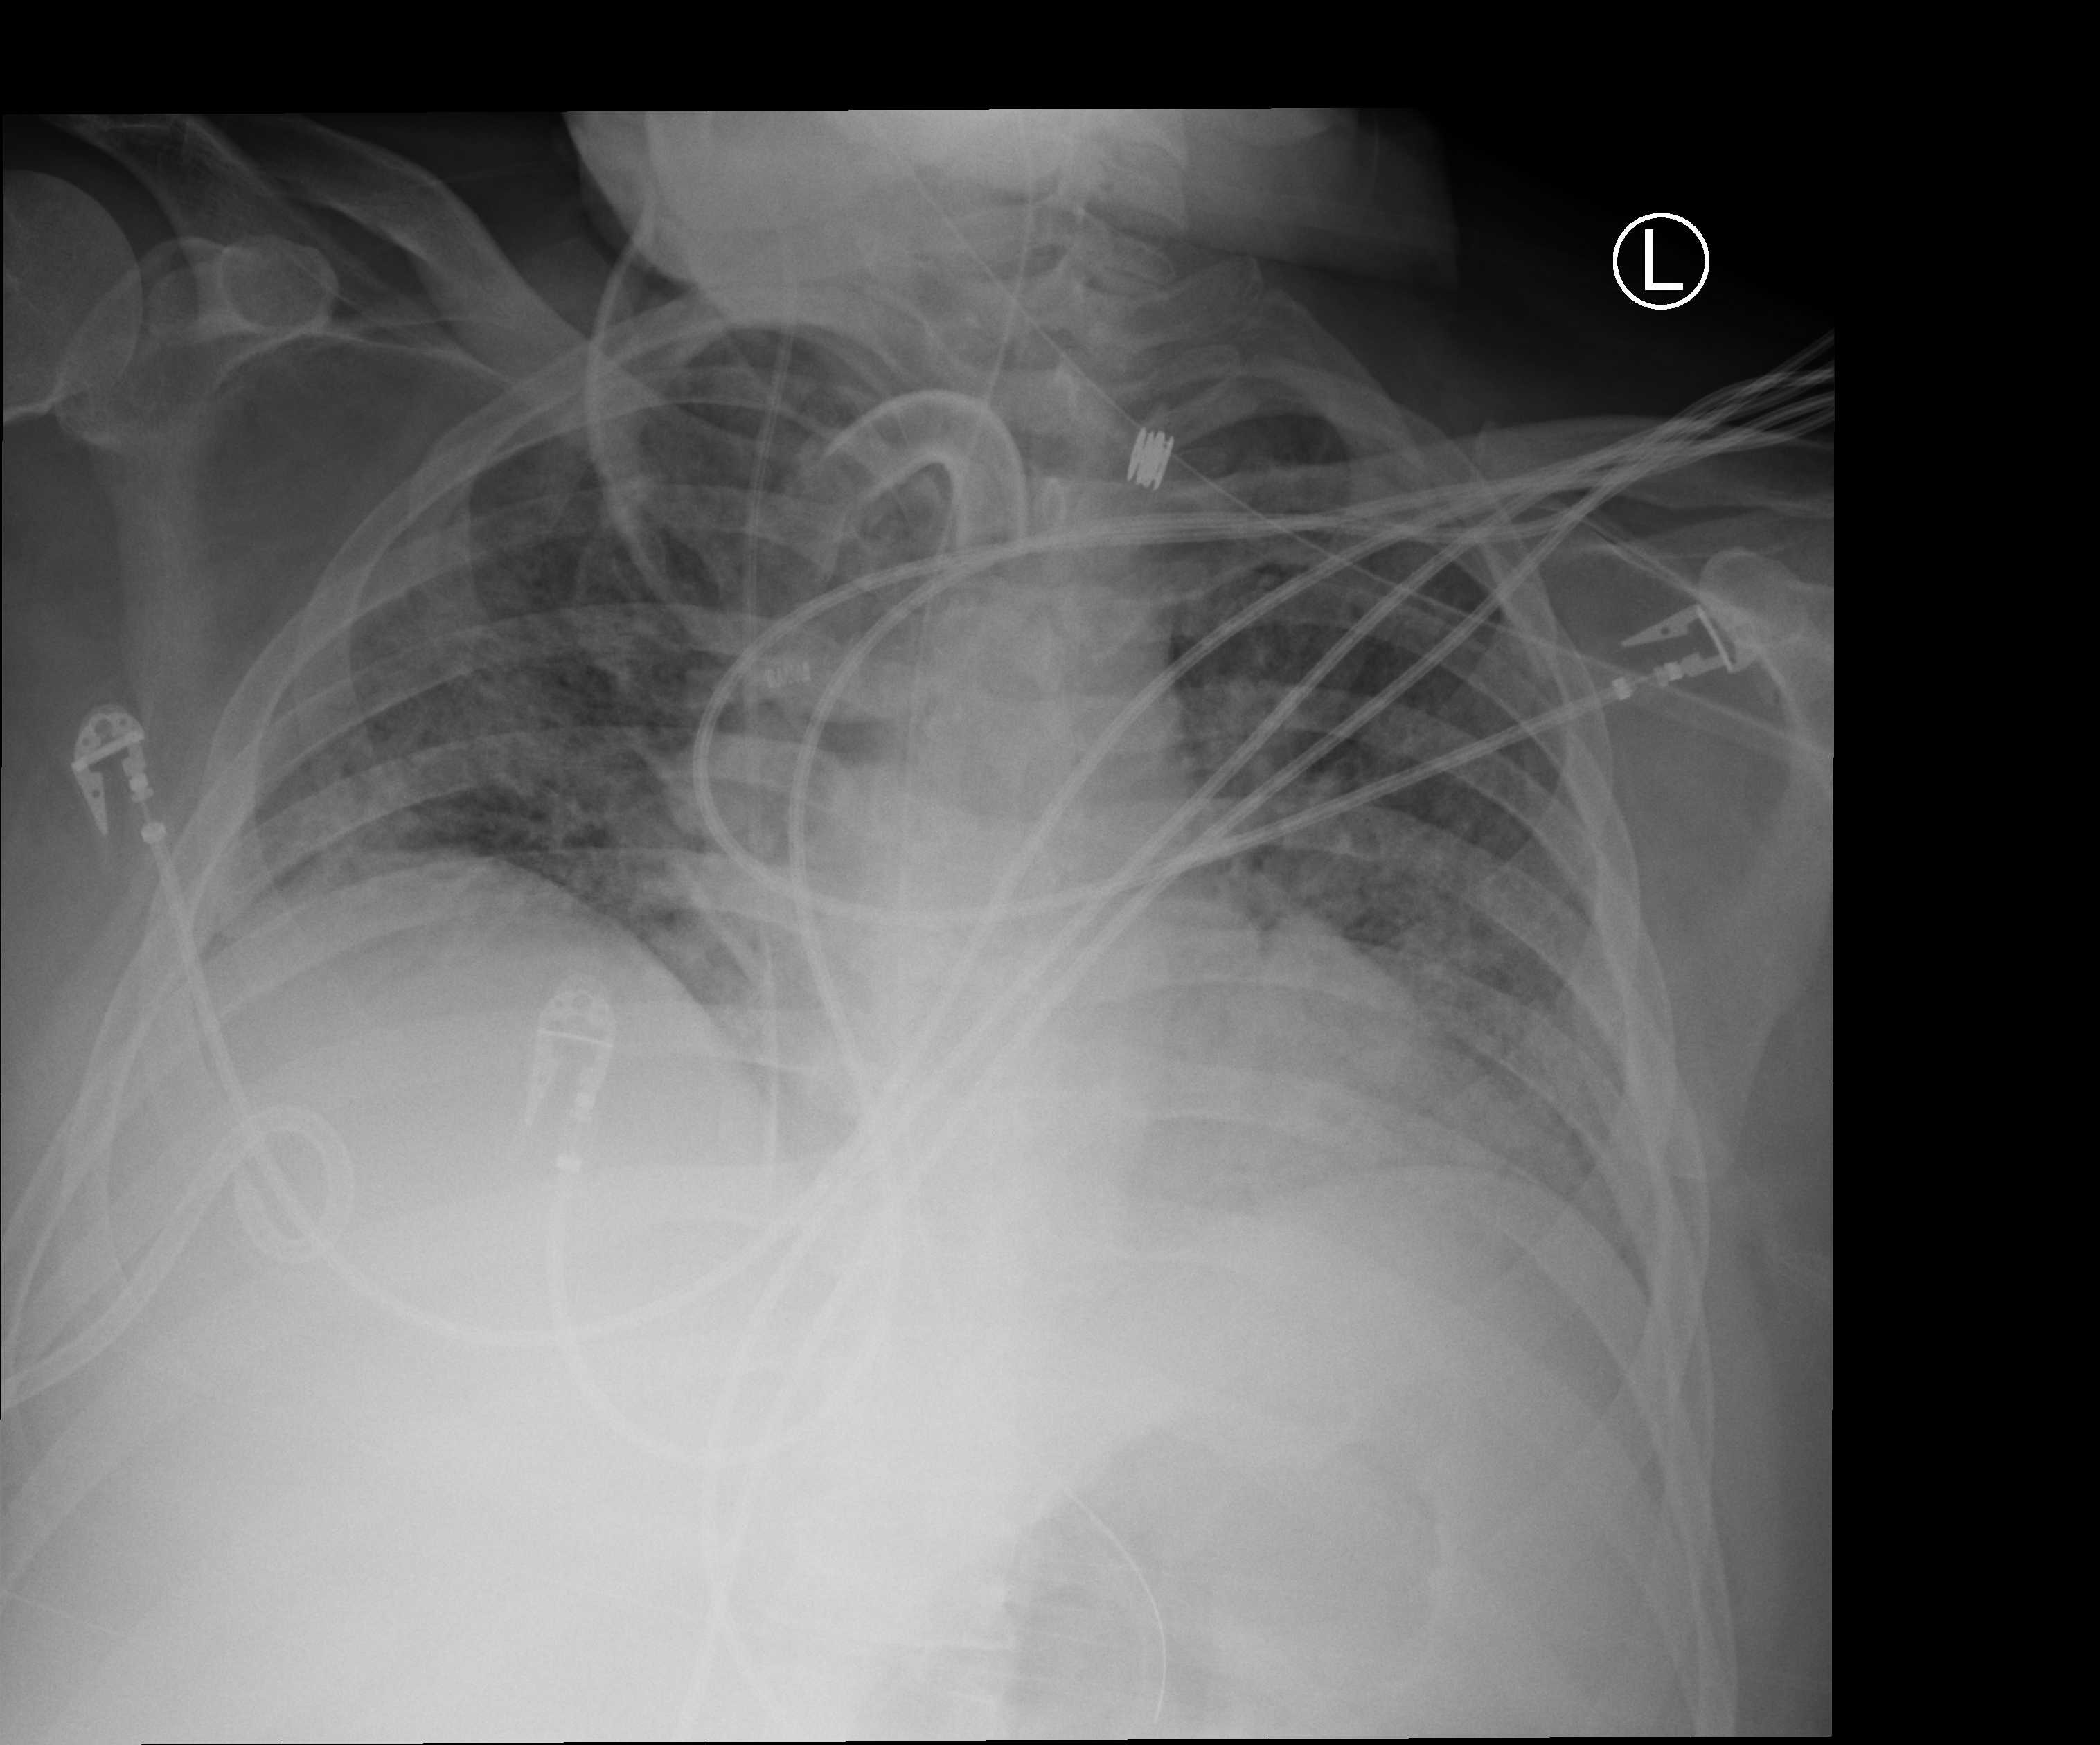
Portable chest radiograph, anteroposterior (AP) projection. Male patient hospitalised with COVID-19, age 18–59 years.
Hospital-stay facts (about this admission, not read from this image; timing relative to this image not recorded): mechanically ventilated during this hospital stay: yes; other chronic lung disease (admission record): no; admitted to intensive care during this hospital stay: yes.